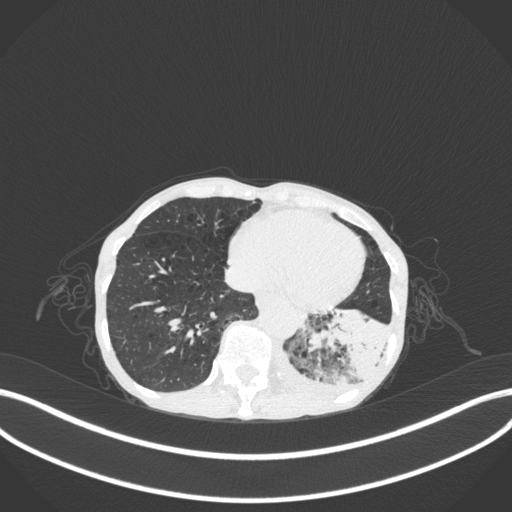
Chest CT, one axial slice; position 57 of 347 along the scan axis; reconstruction kernel B31f; lung window (W 1500 / L -600 HU); 1 mm slice thickness; 512 × 512 image matrix. Female patient, age 70 years. Case-level facts recorded for this patient, not image findings: clinical TNM (as recorded): T3 N0 M0; histopathological grade: G3.
Structures marked on this image (rectangle marked by the reading radiologist):
- lung tumour (recorded histology: small cell carcinoma): box from (x=307, y=296) to (x=394, y=393) px